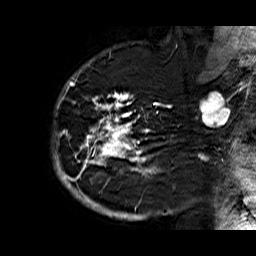
Breast MRI (dynamic contrast-enhanced), one sagittal slice. Slice 47 of 60 in the series (ordered by position). Dynamic contrast-enhanced series, time point 2 of 6 at this slice position (early post-contrast). 1.5 T. TE 6.3 ms, TR 32.9 ms. 4 mm slice thickness. 256 × 256 image matrix, field of view 200 × 200 mm. Female patient. Case-level facts recorded for this patient, not image findings: setting: breast cancer imaged before/during neoadjuvant chemotherapy; receptor status: HR-positive, HER2-negative.
Structures marked on this image (semi-automatic segmentation, software-assisted and operator-edited):
- analysis volume of interest (the breast-tissue region the enhancement analysis was run in; not a lesion): bounding box <52,74,176,210> (left, top, right, bottom; pixels)
- tumour enhancement mask (voxels above the 100 % enhancement threshold inside the analysis volume of interest): <54,74,160,210>